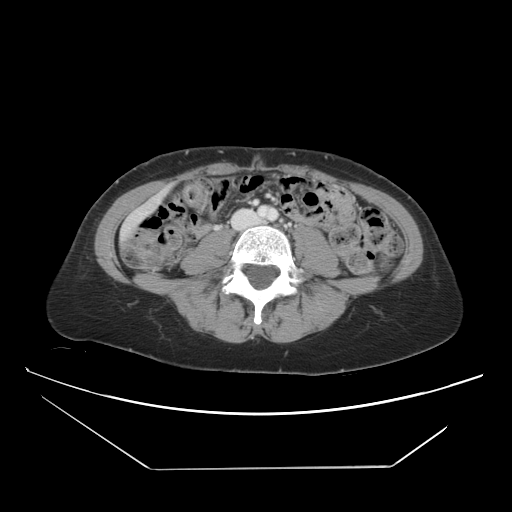
Contrast-enhanced abdominal CT, one axial slice; position 6 of 42 along the scan axis; 120 kVp; intravenous contrast given; soft-tissue window (W 400 / L 40 HU); 5 mm slice thickness; 512 × 512 image matrix, field of view 399 × 399 mm. Female patient, age 52 years. From the clinical record (not read from this slice): diagnosis: colorectal cancer liver metastases, imaged before liver resection.
Outlined on this slice (manually delineated by an expert):
- liver: bounding box <127,196,162,233> (left, top, right, bottom; pixels)
- planned liver remnant (the part of the liver to remain after resection): <131,195,163,223>
- portal vein (with intrahepatic branches): <253,201,258,204>